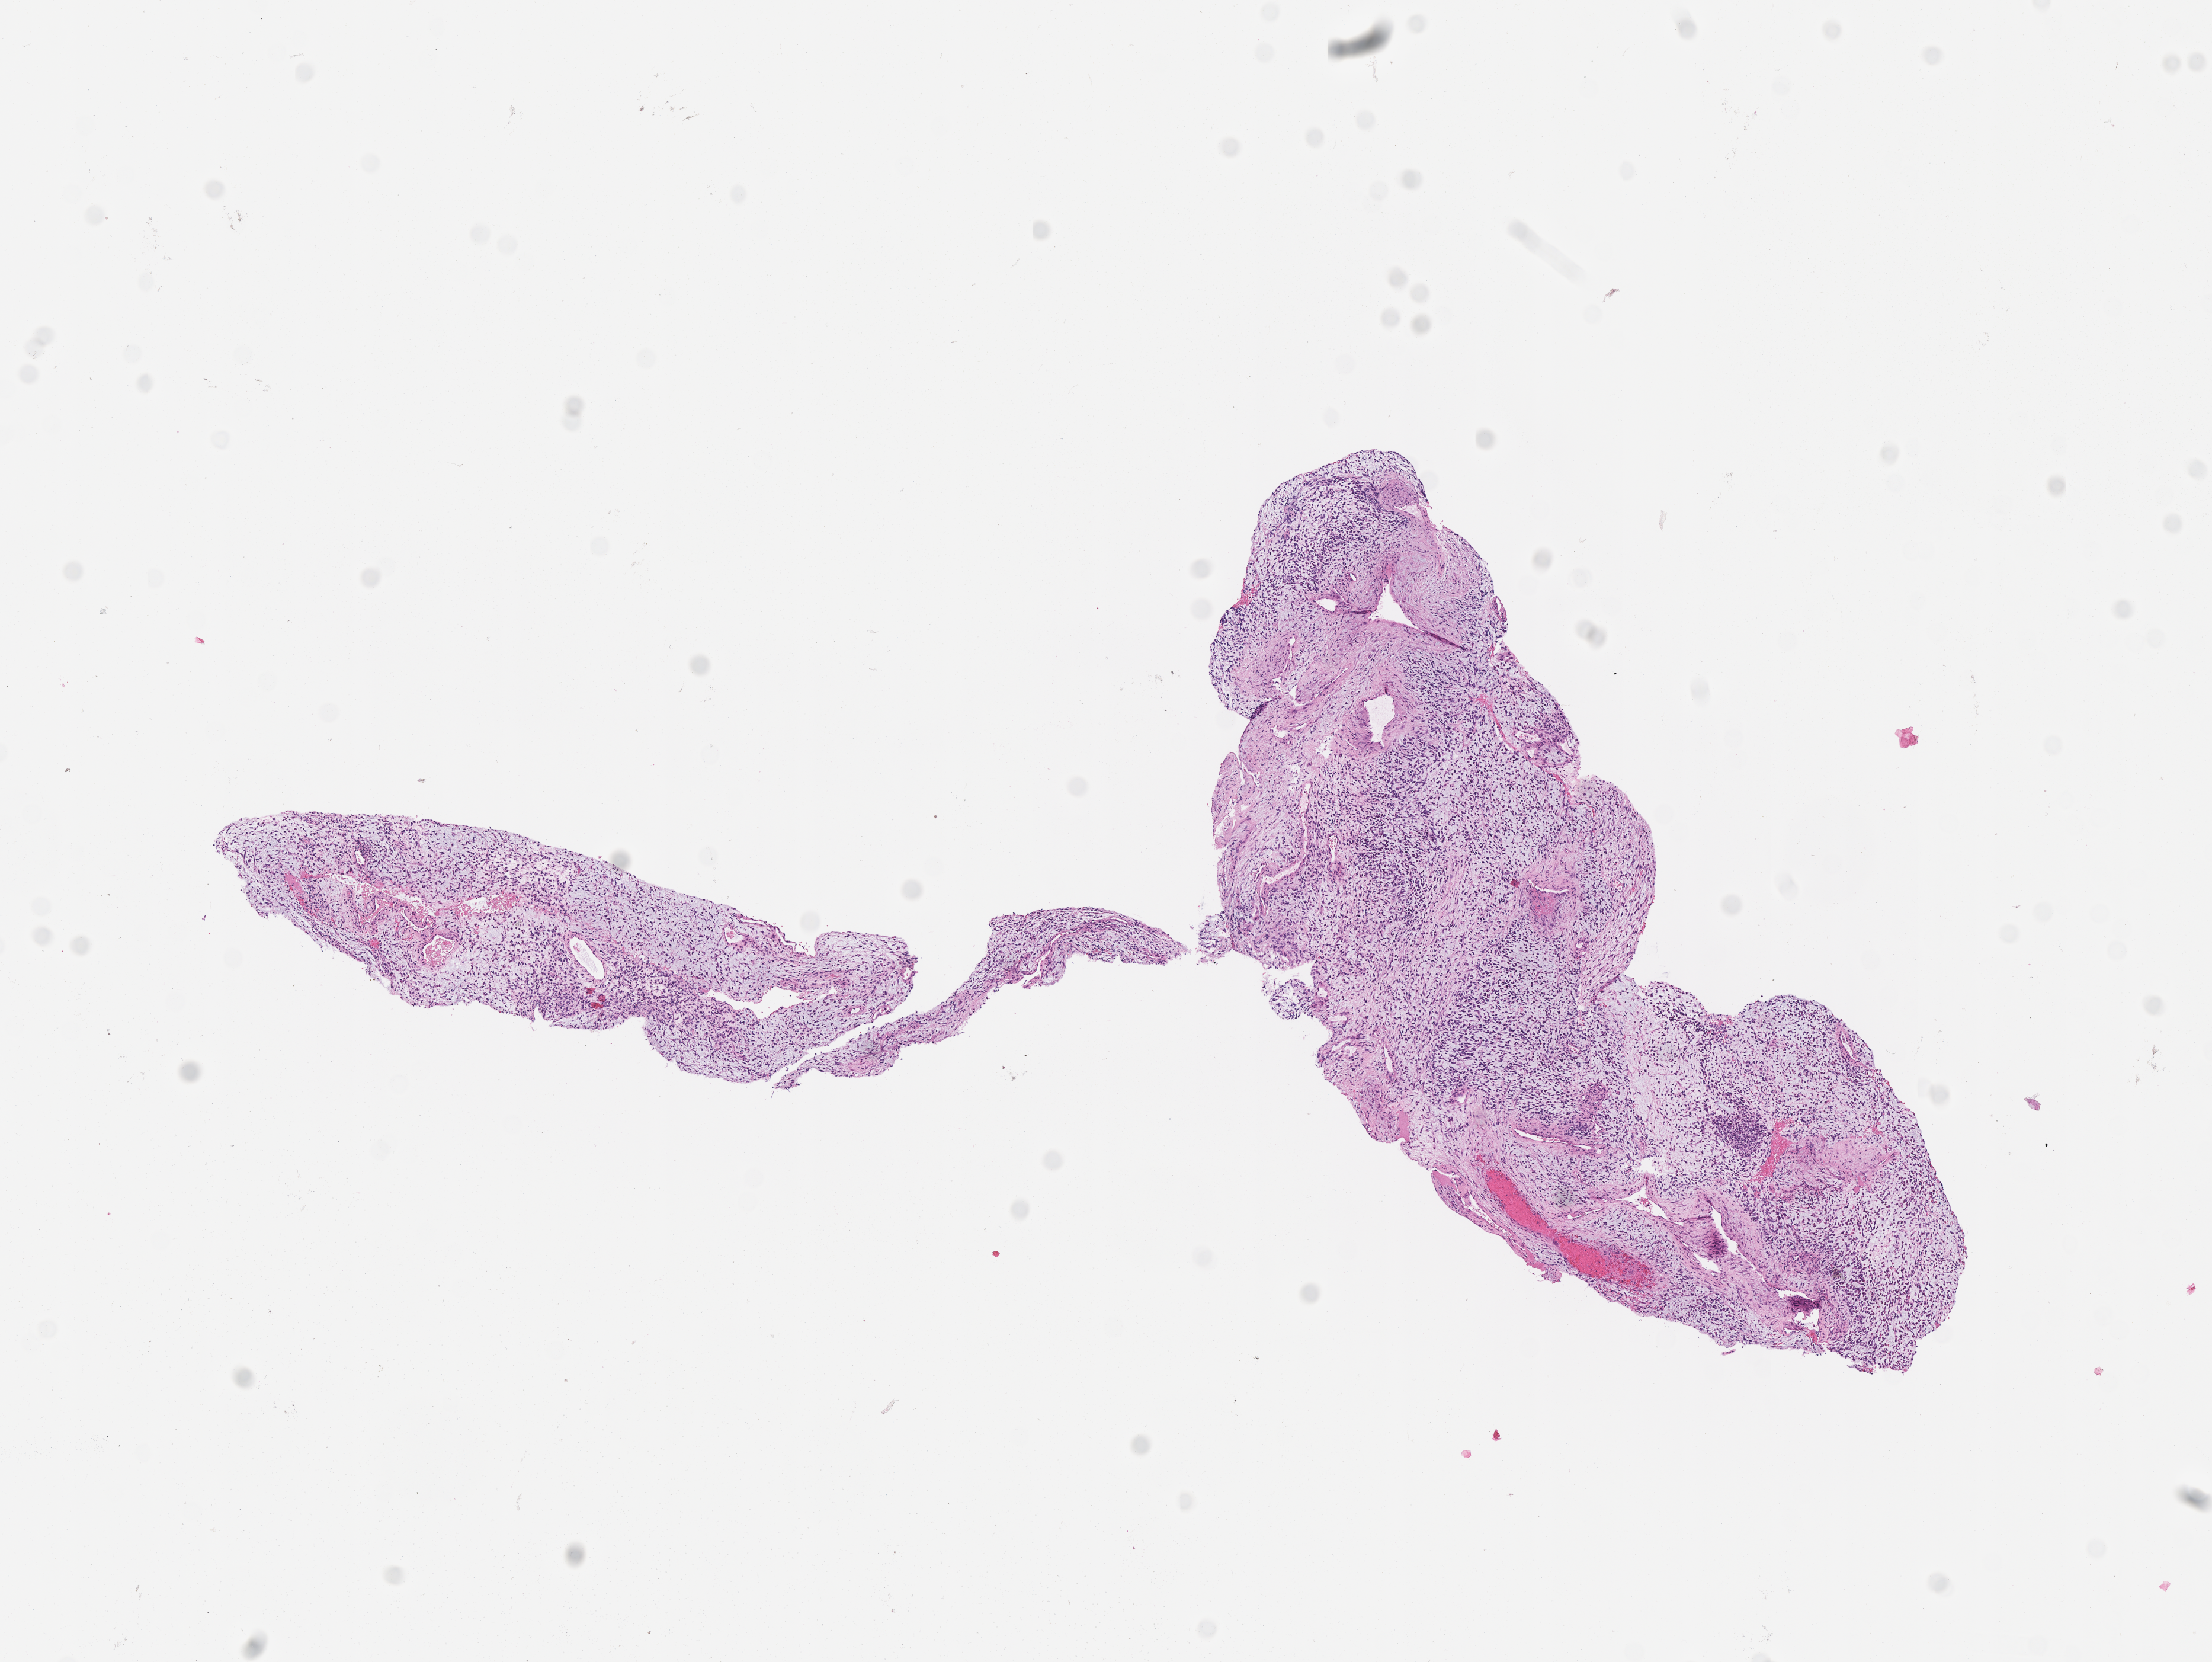
Whole-slide image, haematoxylin and eosin stain of tumor tissue, whole scanned area (about 7.5 x 5.7 mm) shown as a low-resolution overview; FFPE section; sample anatomic site: skull Base, Right. Patient: female, age 3.7 years at diagnosis.
Diagnosis: rhabdomyosarcoma; histological classification: embryonal rhabdomyosarcoma.